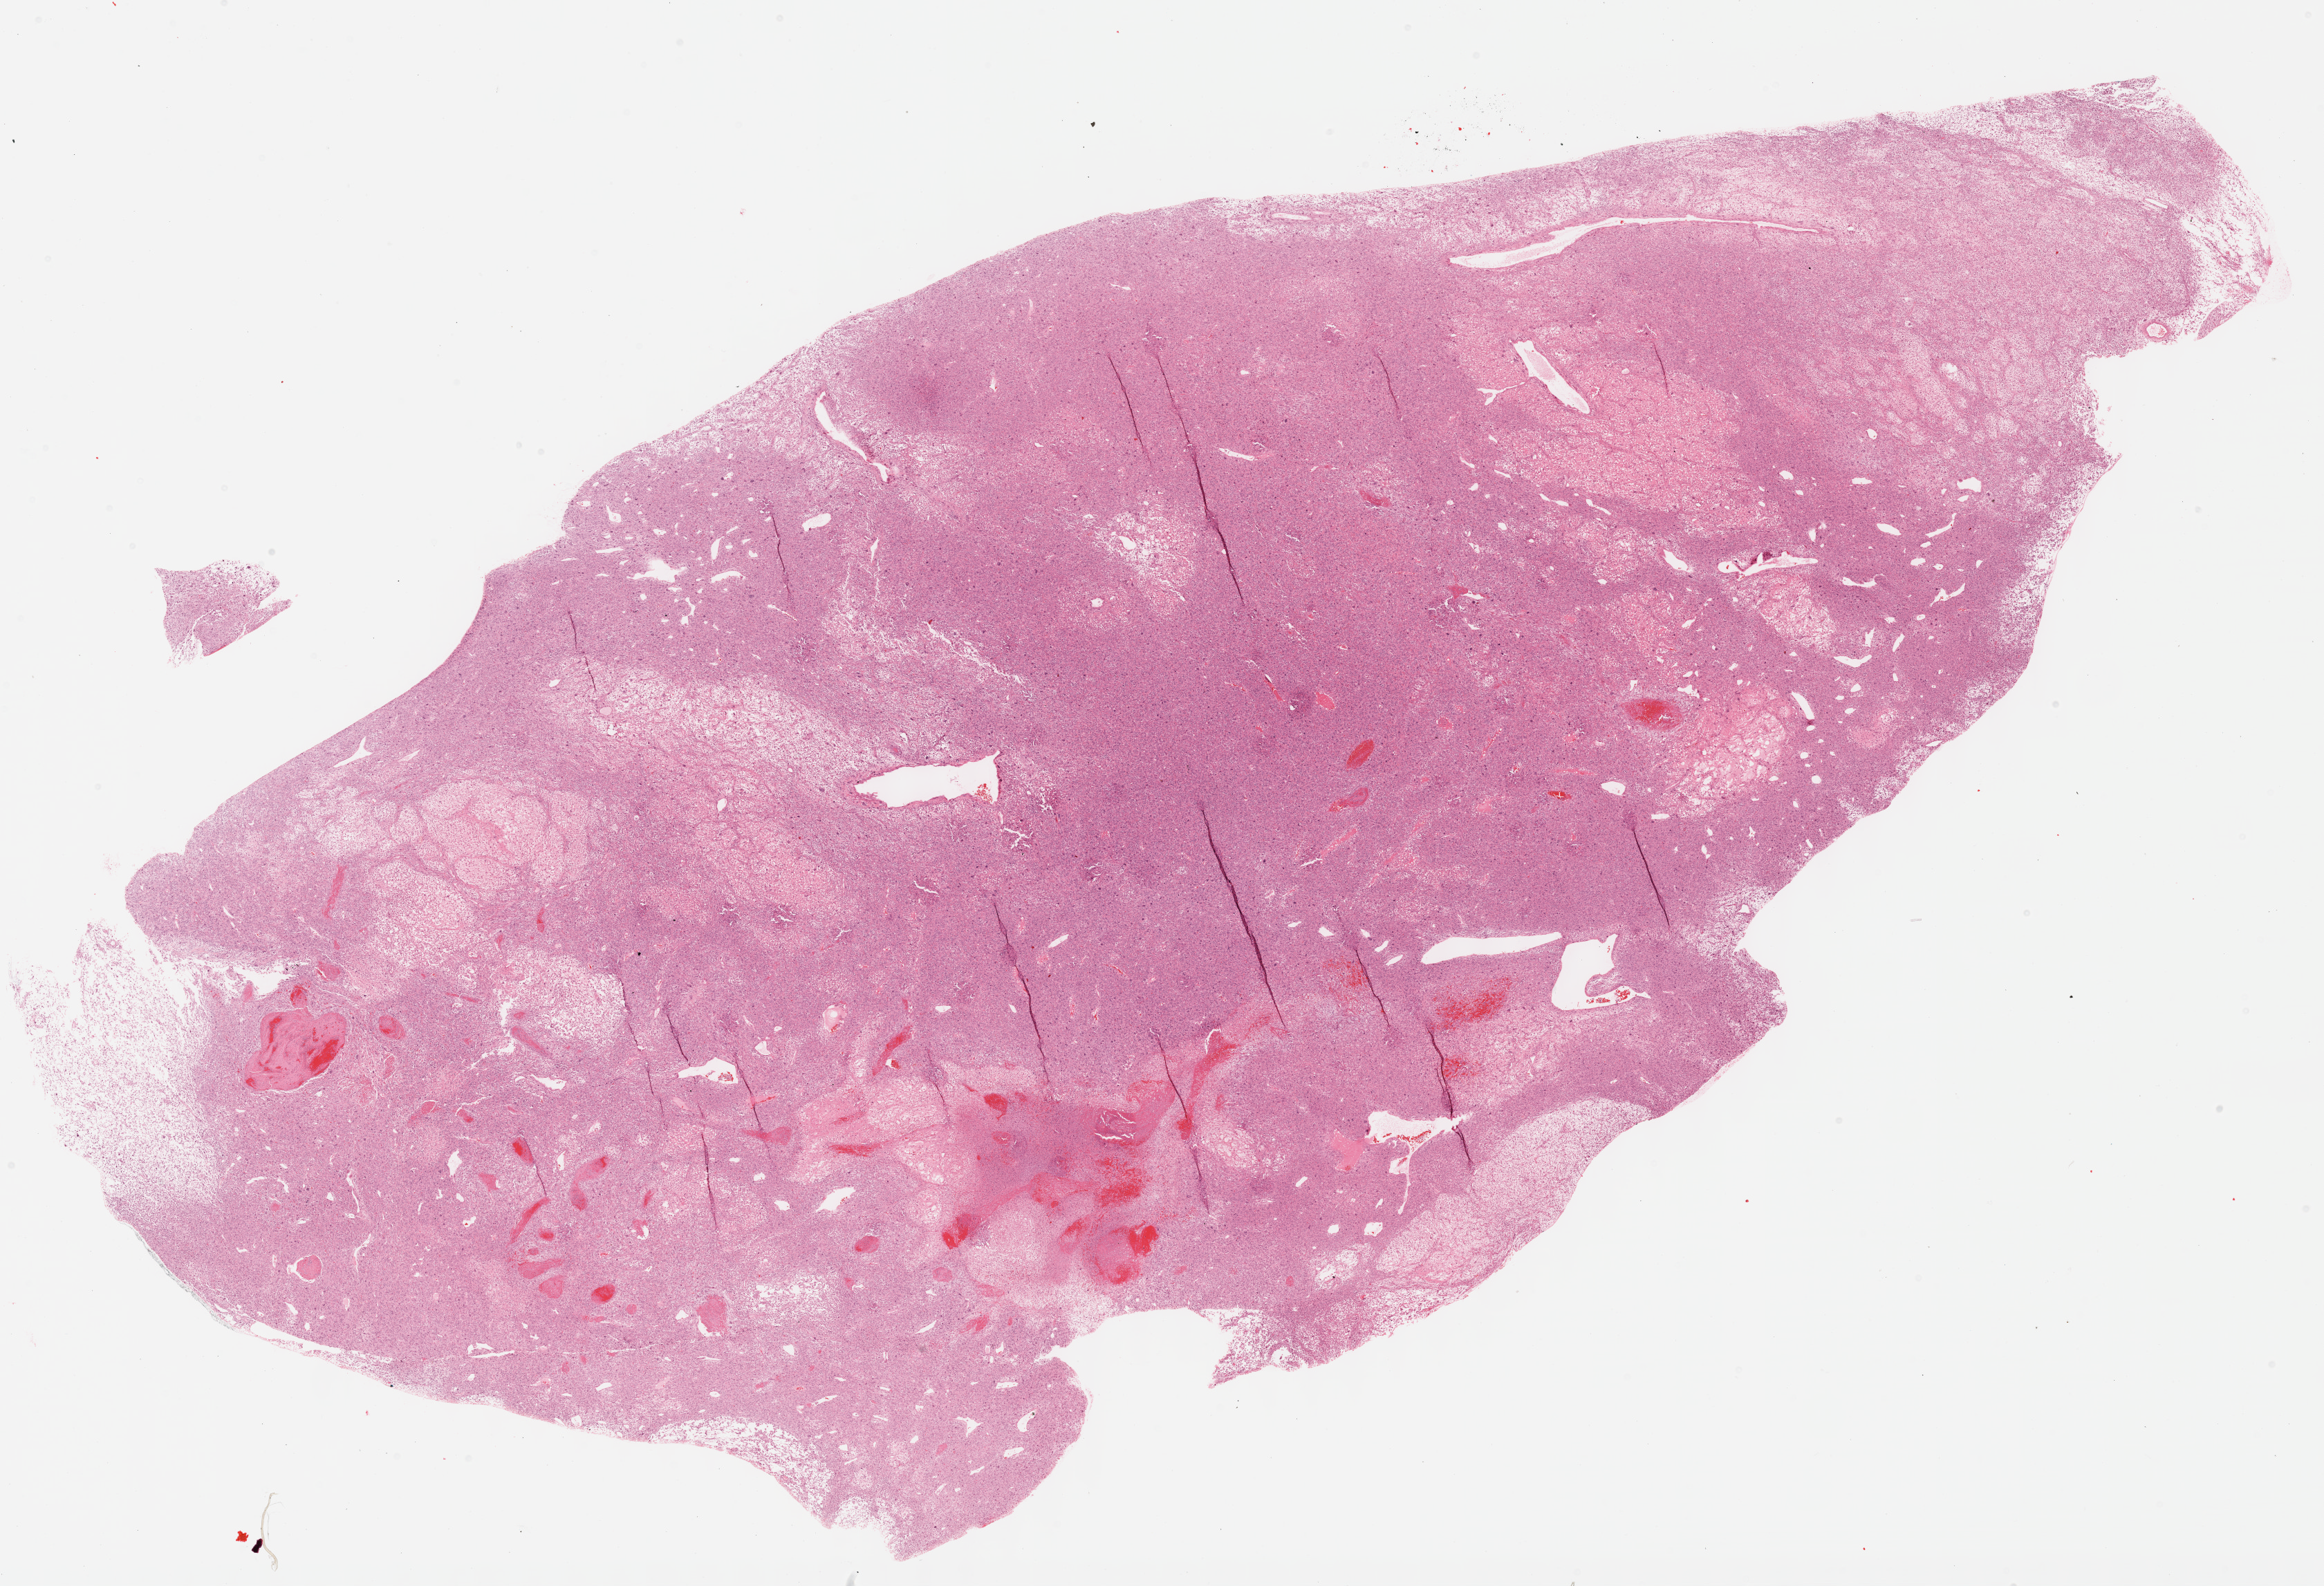
Digitized Hematoxylin and eosin (H&E) stained tissue section (whole slide) — whole scanned area (about 27.2 x 18.5 mm, from a 40x scan) shown as a low-resolution overview. Formalin-fixed paraffin-embedded (FFPE) diagnostic section. Connective, subcutaneous and other soft tissues, primary tumour sample. Female patient; age at initial diagnosis 63 years.
Pathologic diagnosis: Malignant fibrous histiocytoma (connective, subcutaneous and other soft tissues of lower limb and hip).